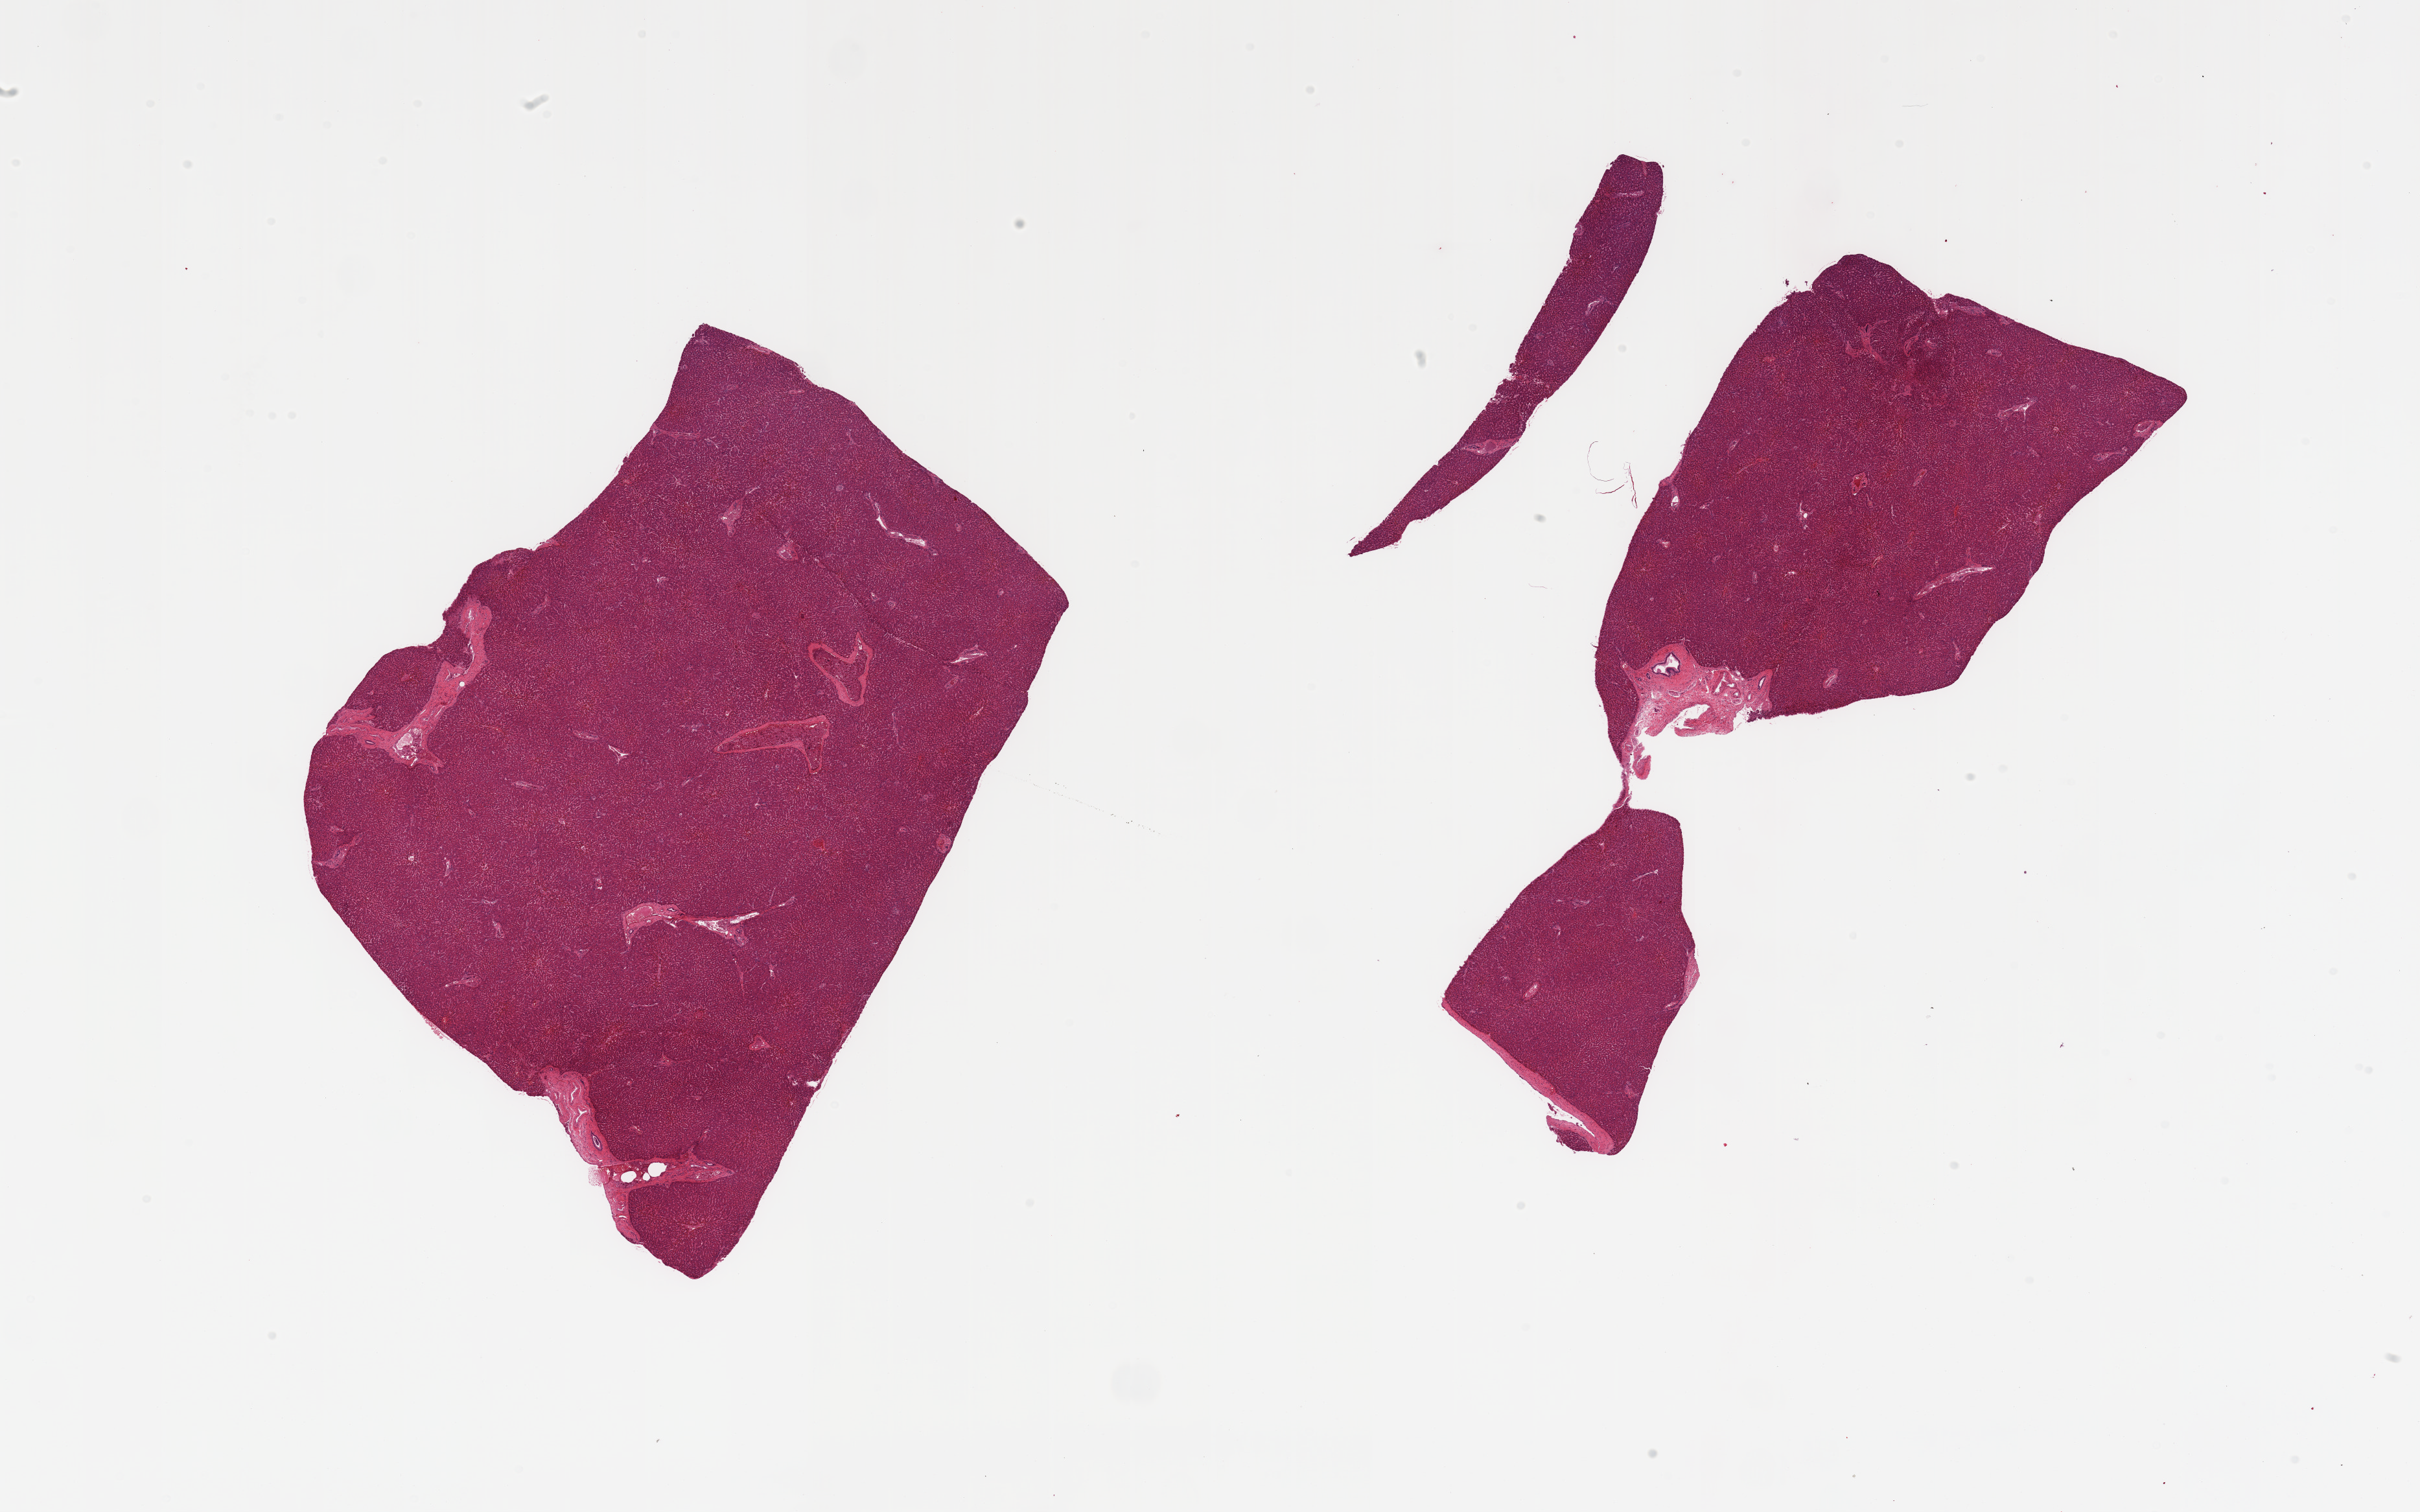
Digitized H&E-stained section, low-resolution overview of the scanned area, about 29.5 x 18.5 mm, PAXgene-fixed, paraffin-embedded tissue, sampled site (target tissue): liver, tissue donor sample. Donor: male.
- pathologist's review note for this sample: 3 pieces